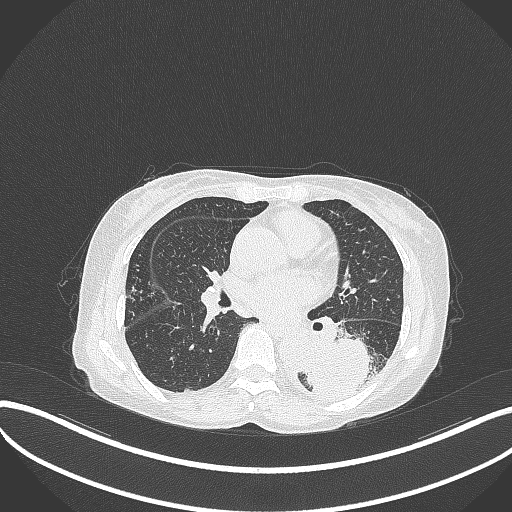
Chest CT, one axial slice. Position 156 of 370 along the scan axis. Reconstruction kernel B70f. 120 kVp. Lung window (W 1500 / L -600 HU). 512 × 512 image matrix. Female patient, age 78 years. From the clinical record (not read from this slice): clinical TNM (as recorded): T3 N0 M1.
Structures marked on this image (rectangle marked by the reading radiologist):
- lung tumour (recorded histology: squamous cell carcinoma): bounding box [x1, y1, x2, y2] px = [305, 332, 391, 401]